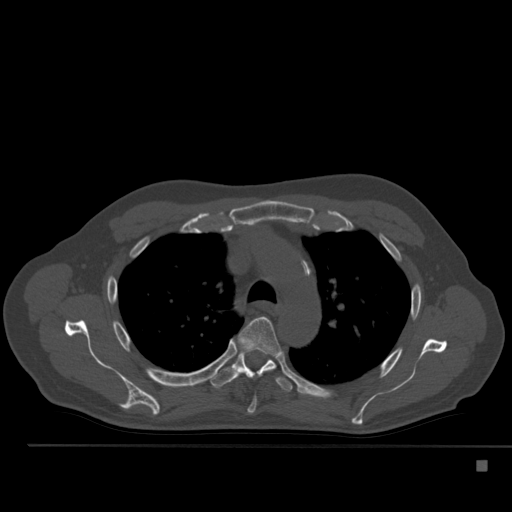
CT including the spine, one axial slice; position 374 of 517 along the scan axis; 120 kVp; bone window (W 1800 / L 400 HU); 1.5 mm slice thickness; 512 × 512 image matrix, field of view 408 × 408 mm. Male patient, age 70 years. Case-level facts recorded for this patient, not image findings: primary cancer: renal; vertebrae with lytic lesions (as recorded): T4, T6, T10, T12, L3, L4, L5.
Structures marked on this image (semi-automatically segmented with operator editing):
- T4 vertebra: bounding box (x1, y1, x2, y2) in pixels: (237, 317, 287, 414)
- T5 vertebra: (210, 350, 293, 392)